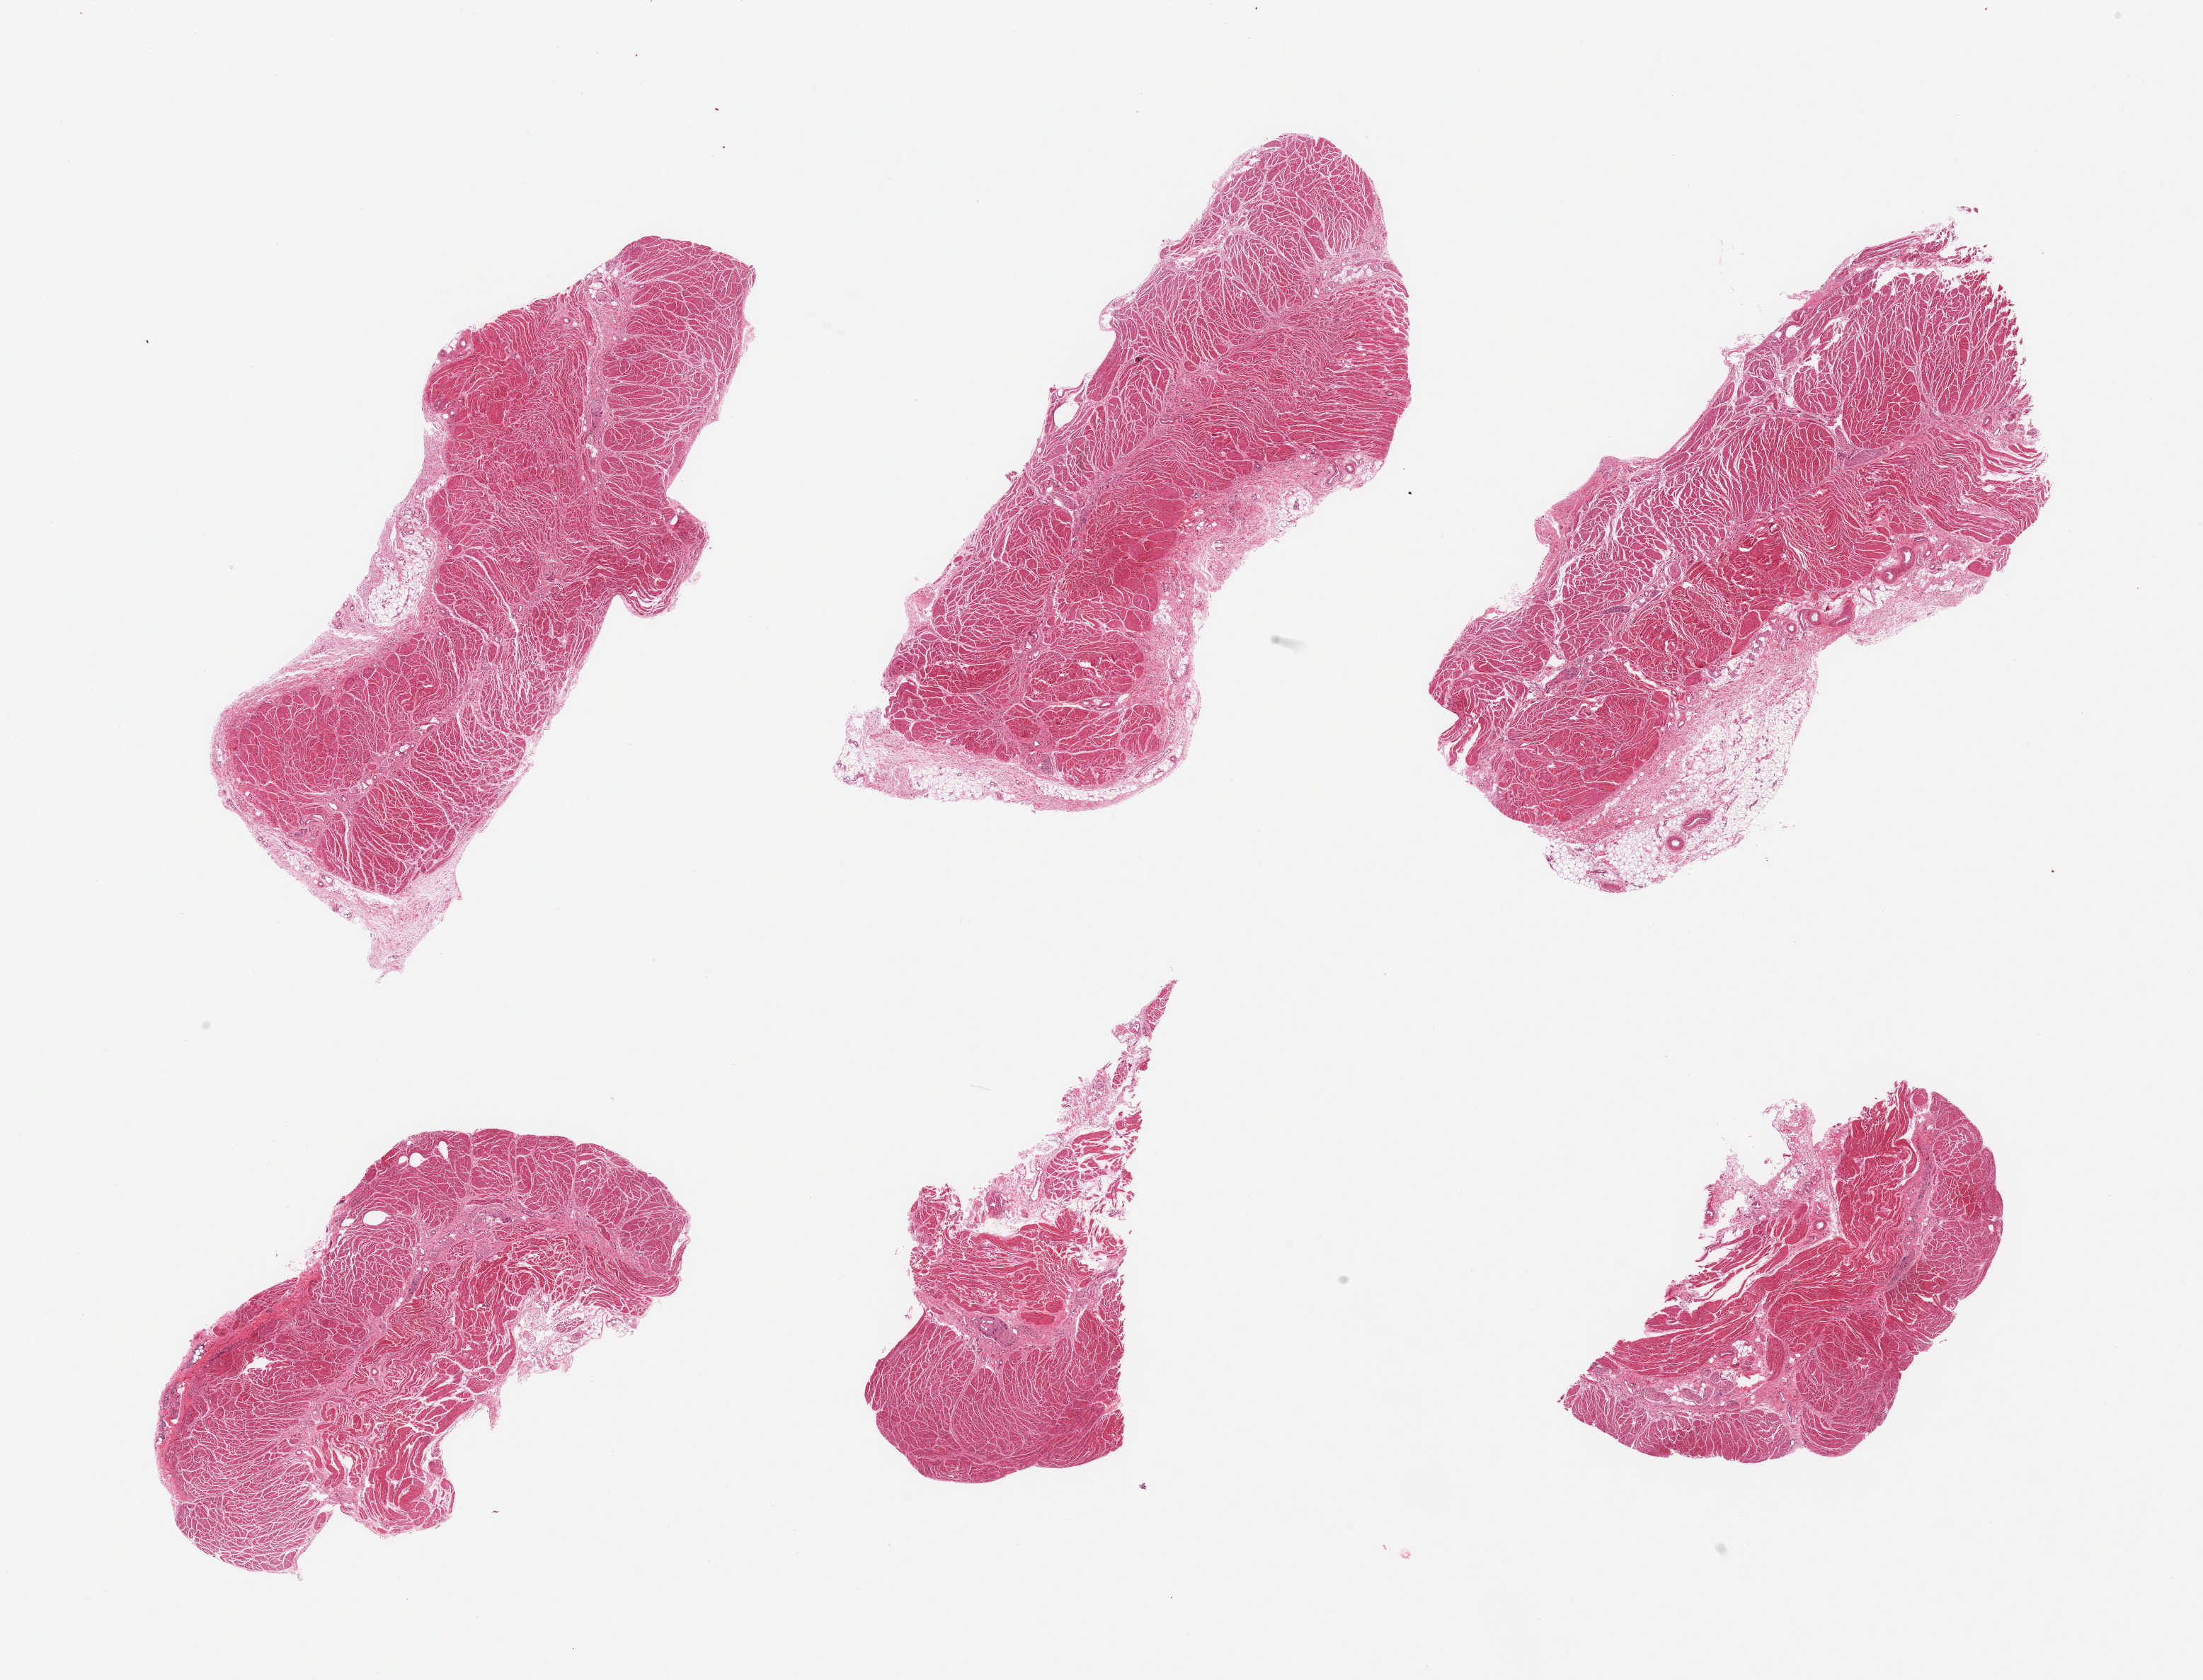
H&E whole-slide image, shown as a low-resolution overview of the whole scanned area (about 24.6 x 18.8 mm); PAXgene-fixed, paraffin-embedded tissue; target tissue: gastroesophageal junction; donor tissue sample. Donor: male.
• review note (as recorded): 6 pieces; target muscularis with up to 20% attached fat